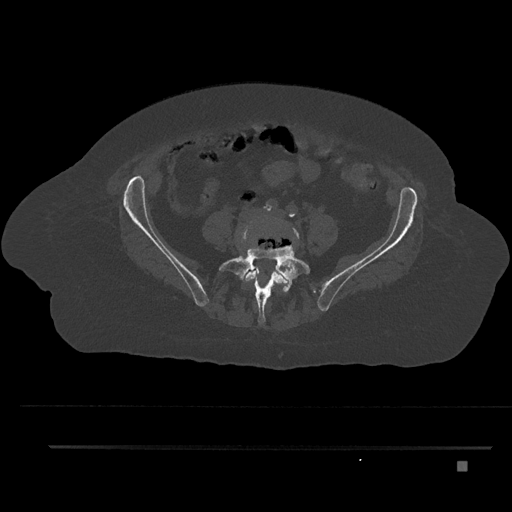
CT including the spine, one axial slice. Position 50 of 797 along the scan axis. Reconstruction kernel Br40s/3. 120 kVp. Bone window (W 1800 / L 400 HU). 512 × 512 image matrix, field of view 437 × 437 mm. Female patient, age 76 years. Case-level facts recorded for this patient, not image findings: primary cancer: lung.
Structures marked on this image (semi-automatically segmented with operator editing):
- L4 vertebra: bounding box <238,218,300,307> (left, top, right, bottom; pixels)
- L5 vertebra: <219,247,311,324>